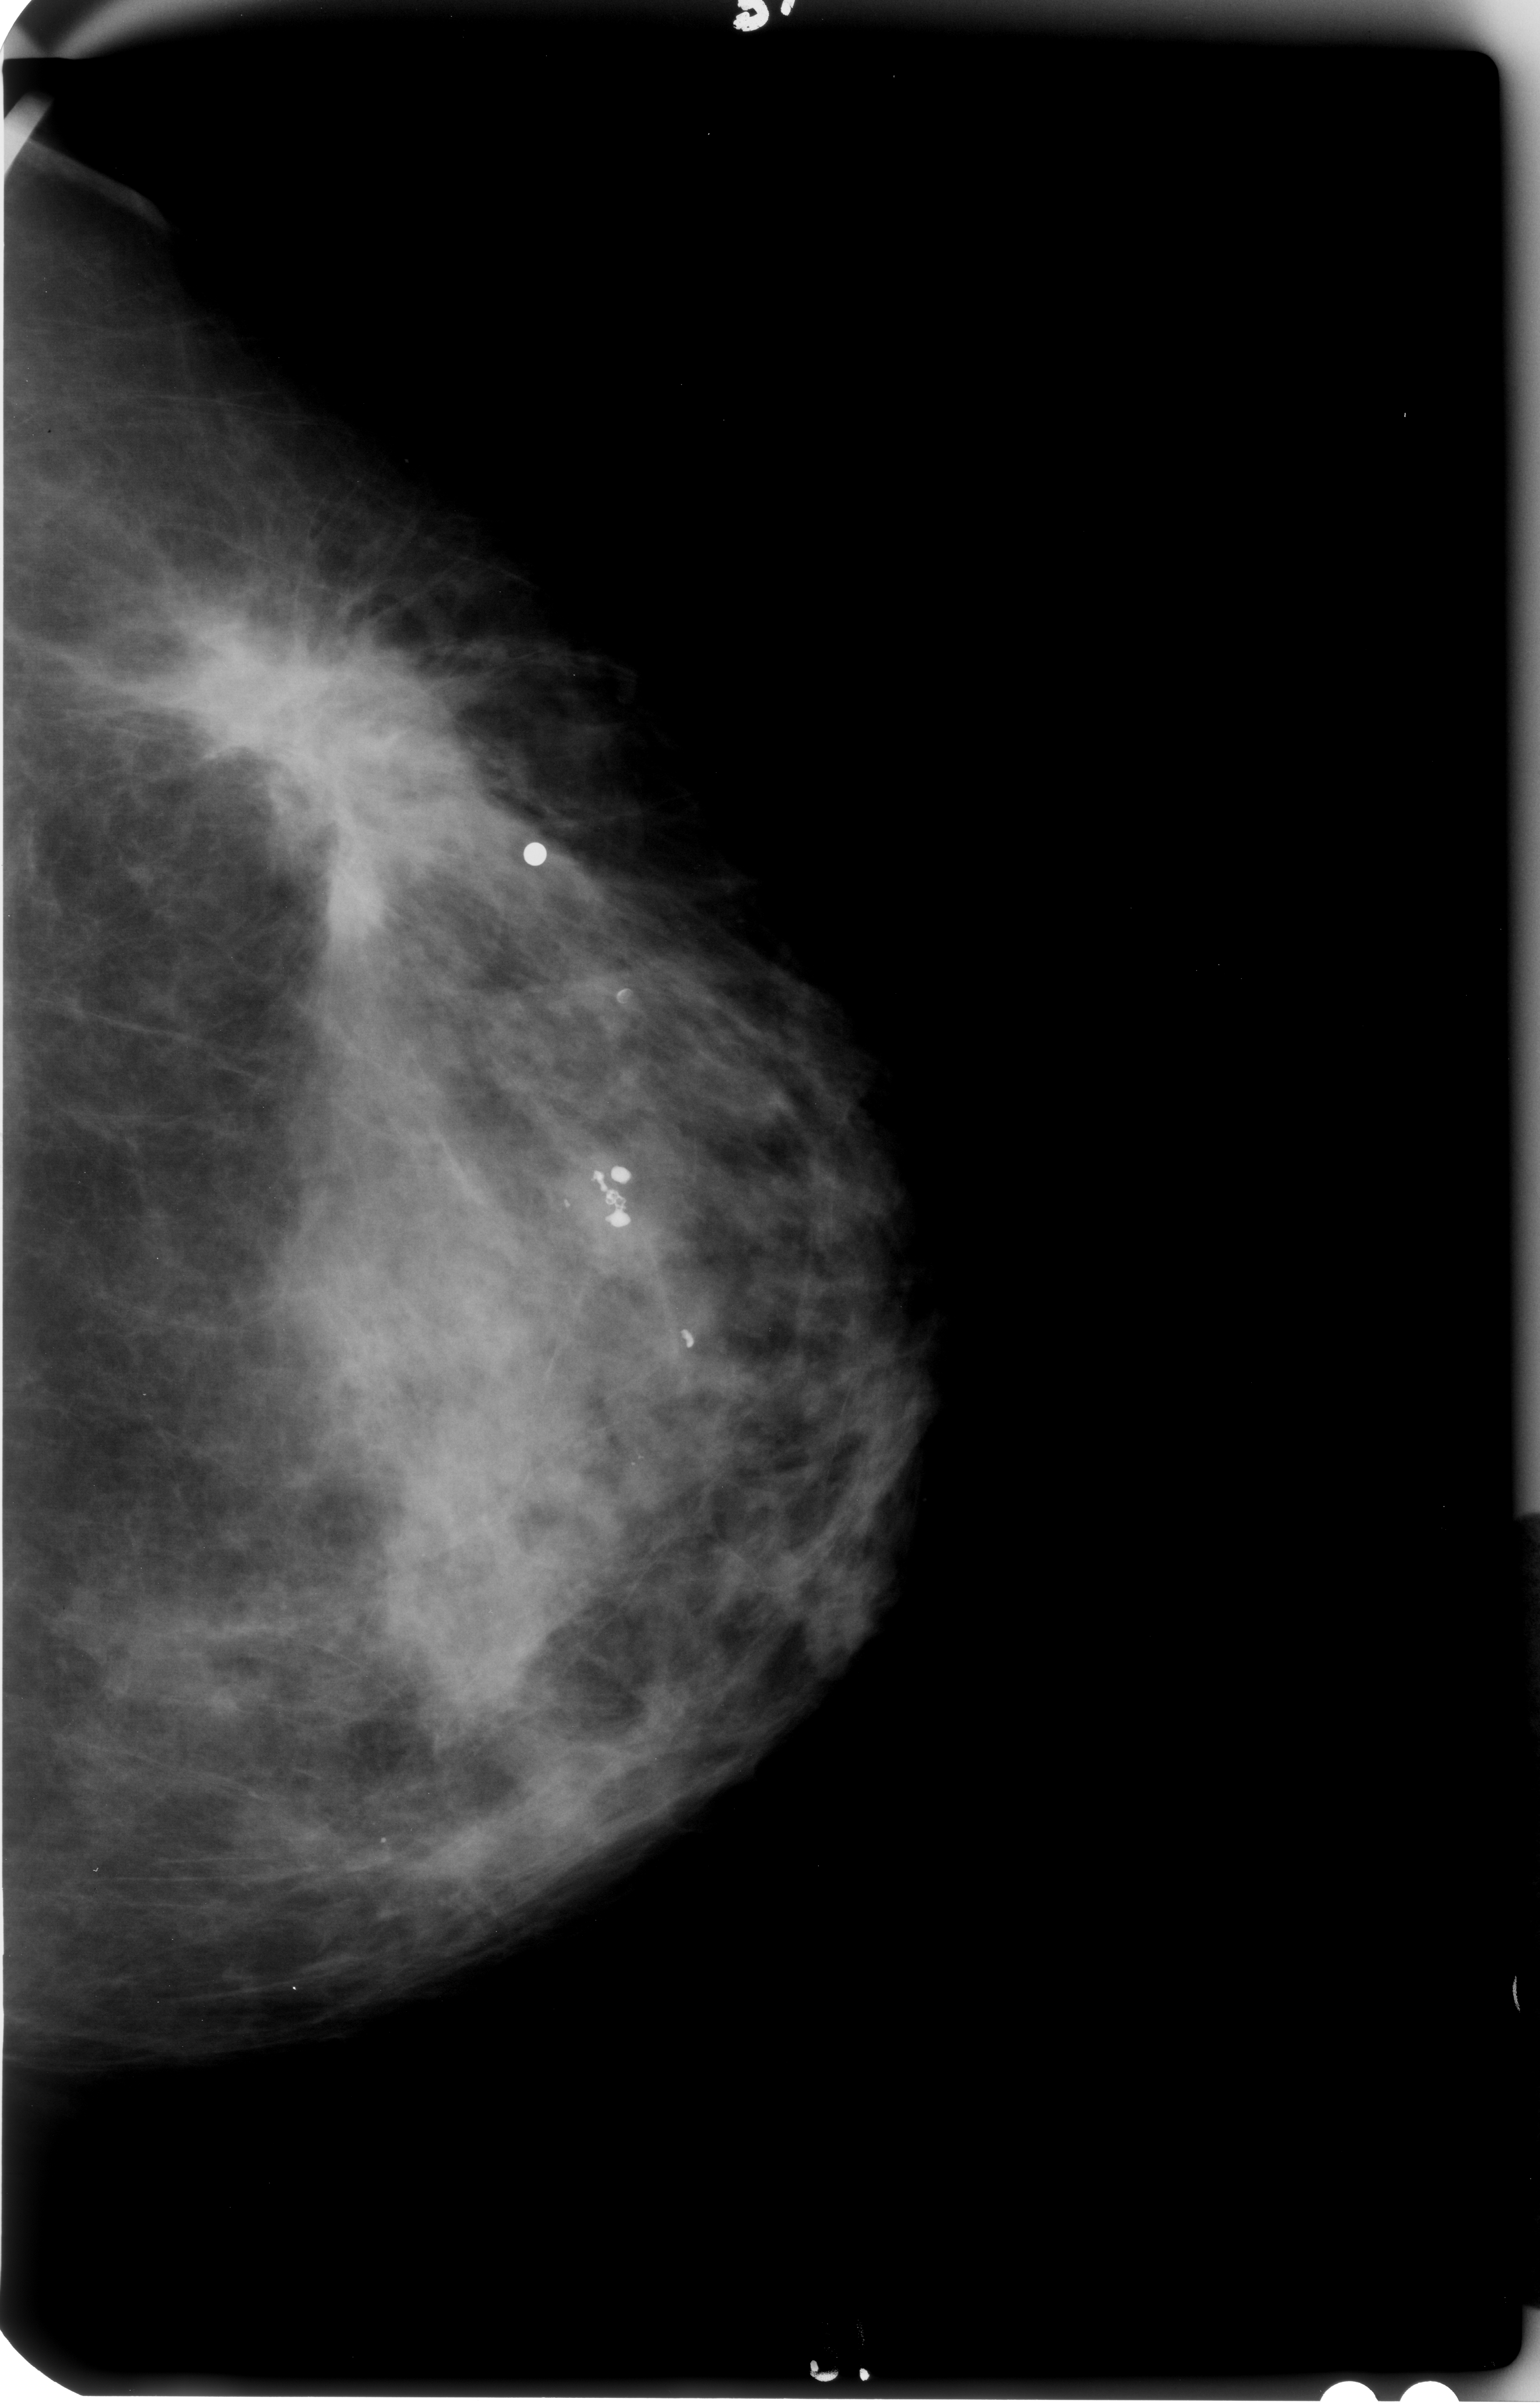
Digitized screen-film mammogram. Left breast. CC view. Breast composition: extremely dense (BI-RADS density category 4 of 4). 1540 × 2408 image matrix.
Marked abnormalities (boxes around the expert regions of interest):
- mass, shape irregular / architectural distortion, margins ill defined / spiculated; BI-RADS assessment category 4; subtlety rating 4 on a 1 (subtle) to 5 (obvious) scale; pathology (as recorded): malignant: bounding box [x1, y1, x2, y2] px = [149, 585, 495, 906]